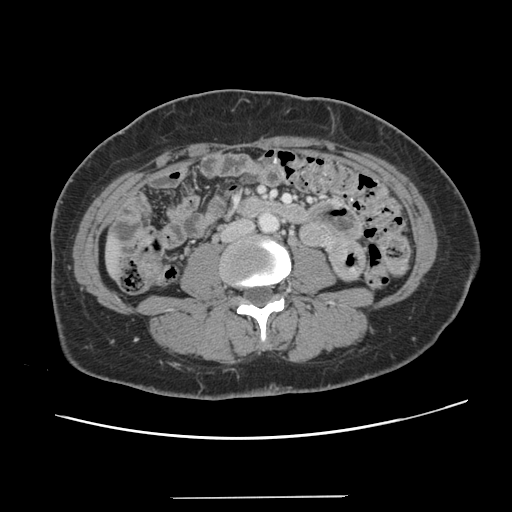
Contrast-enhanced abdominal CT, one axial slice; slice 17 of 141 in the series (ordered by position); 120 kVp; soft-tissue window (W 400 / L 40 HU); 2.5 mm slice thickness; 512 × 512 image matrix, field of view 366 × 366 mm. Female patient, age 53 years. Case-level facts recorded for this patient, not image findings: diagnosis: colorectal cancer liver metastases, imaged before liver resection; multiple liver metastases: no; largest metastasis: 14.5 cm; chemotherapy before resection: yes.
Annotated regions visible in this slice (outlined manually by an expert reader):
- liver: bounding box [x1, y1, x2, y2] px = [107, 238, 122, 274]
- planned liver remnant (the part of the liver to remain after resection): [108, 238, 121, 274]